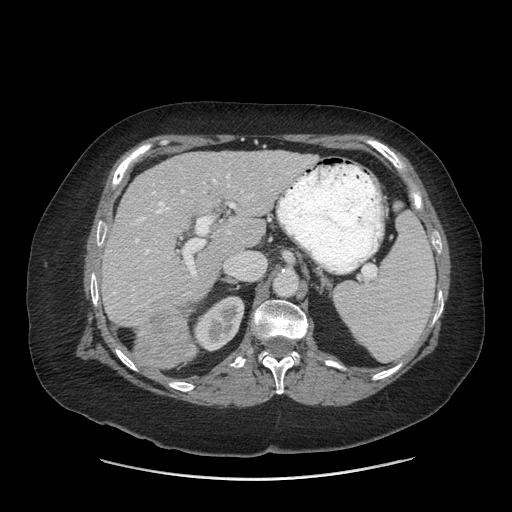
Contrast-enhanced abdominal CT (liver protocol), one axial slice; reconstruction kernel STANDARD; 140 kVp; soft-tissue window (W 400 / L 40 HU); 2.5 mm slice thickness; 512 × 512 image matrix. Case-level facts recorded for this patient, not image findings: diagnosis: hepatocellular carcinoma (patient treated with transarterial chemoembolisation; whether this scan precedes or follows treatment is not stated here); TNM stage (as recorded): Stage-IIIB; Child-Pugh class: A; tumour differentiation: moderately differentiated; tumour nodularity: multinodular.
Outlined on this slice (semi-automatic segmentation, software-assisted and operator-edited):
- liver parenchyma outside the tumour (the mass and vessels are separate outlines, so this box may not span the whole liver): bounding box <102,150,316,360> (left, top, right, bottom; pixels)
- mass: <133,306,195,369>
- liver vessels: <113,175,236,294>